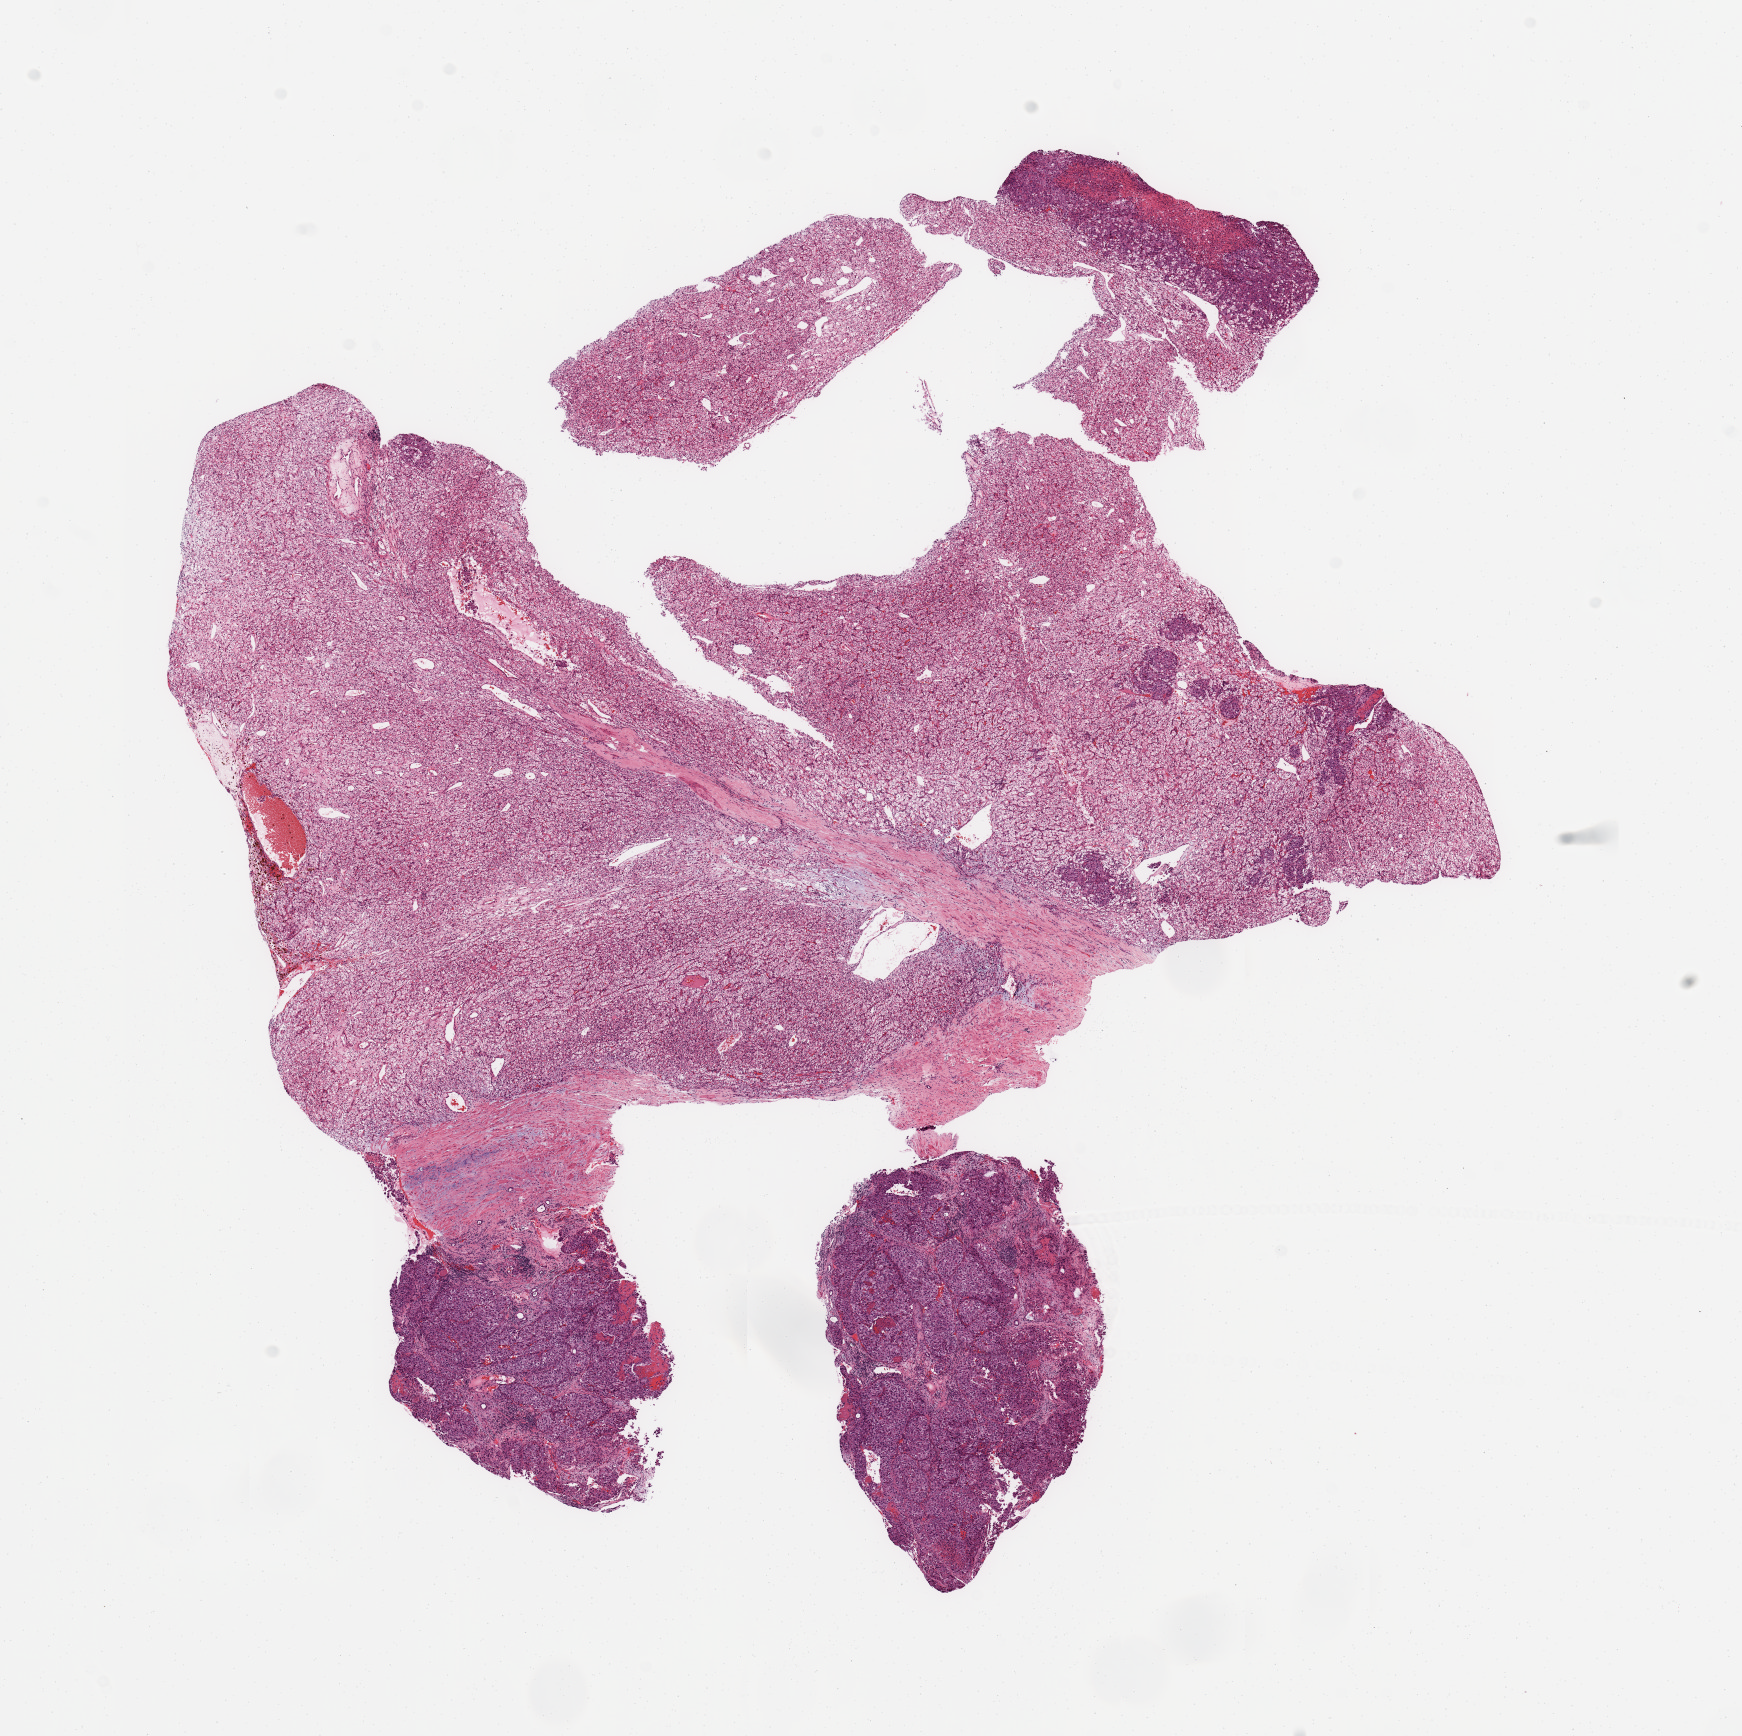
Digitized Hematoxylin and eosin (H&E) stained tissue section (whole slide), low-resolution overview of the scanned area, about 13.8 x 13.7 mm (from a 20x scan). Tumour tissue sample, sampled site: kidney. Patient: male, age 60 years. Histologic grade: G4 (undifferentiated). Composition of this section per pathologist review: tumour nuclei 90%, necrosis 5%.
Histologic diagnosis: Renal cell carcinoma, NOS. AJCC pathologic stage: IV.